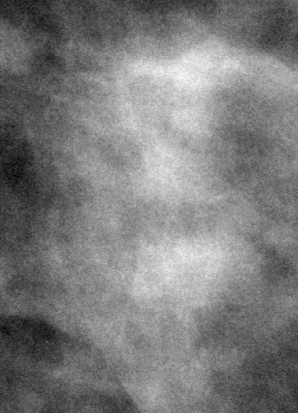
Region of interest cut from a scanned film mammogram (one marked finding), right breast, CC view.
Marked abnormality: mass, shape oval, margins obscured; BI-RADS assessment category 3; subtlety rating 4 on a 1 (subtle) to 5 (obvious) scale; pathology (as recorded): benign.